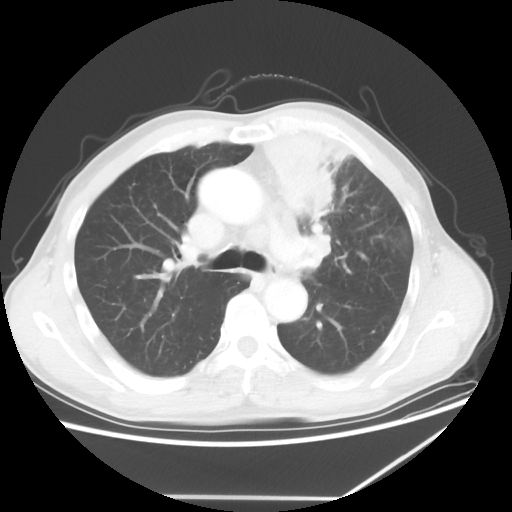
Chest CT, one axial slice. Slice 41 of 64 in the series (ordered by position). 100 kVp. Lung window (W 1500 / L -600 HU). 5 mm slice thickness. 512 × 512 image matrix. Male patient, age 64 years. From the clinical record (not read from this slice): clinical TNM (as recorded): T1c N1 M1.
Annotated regions visible in this slice (bounding box drawn by a radiologist):
- lung tumour (recorded histology: squamous cell carcinoma): bounding box [x1, y1, x2, y2] px = [257, 118, 354, 220]